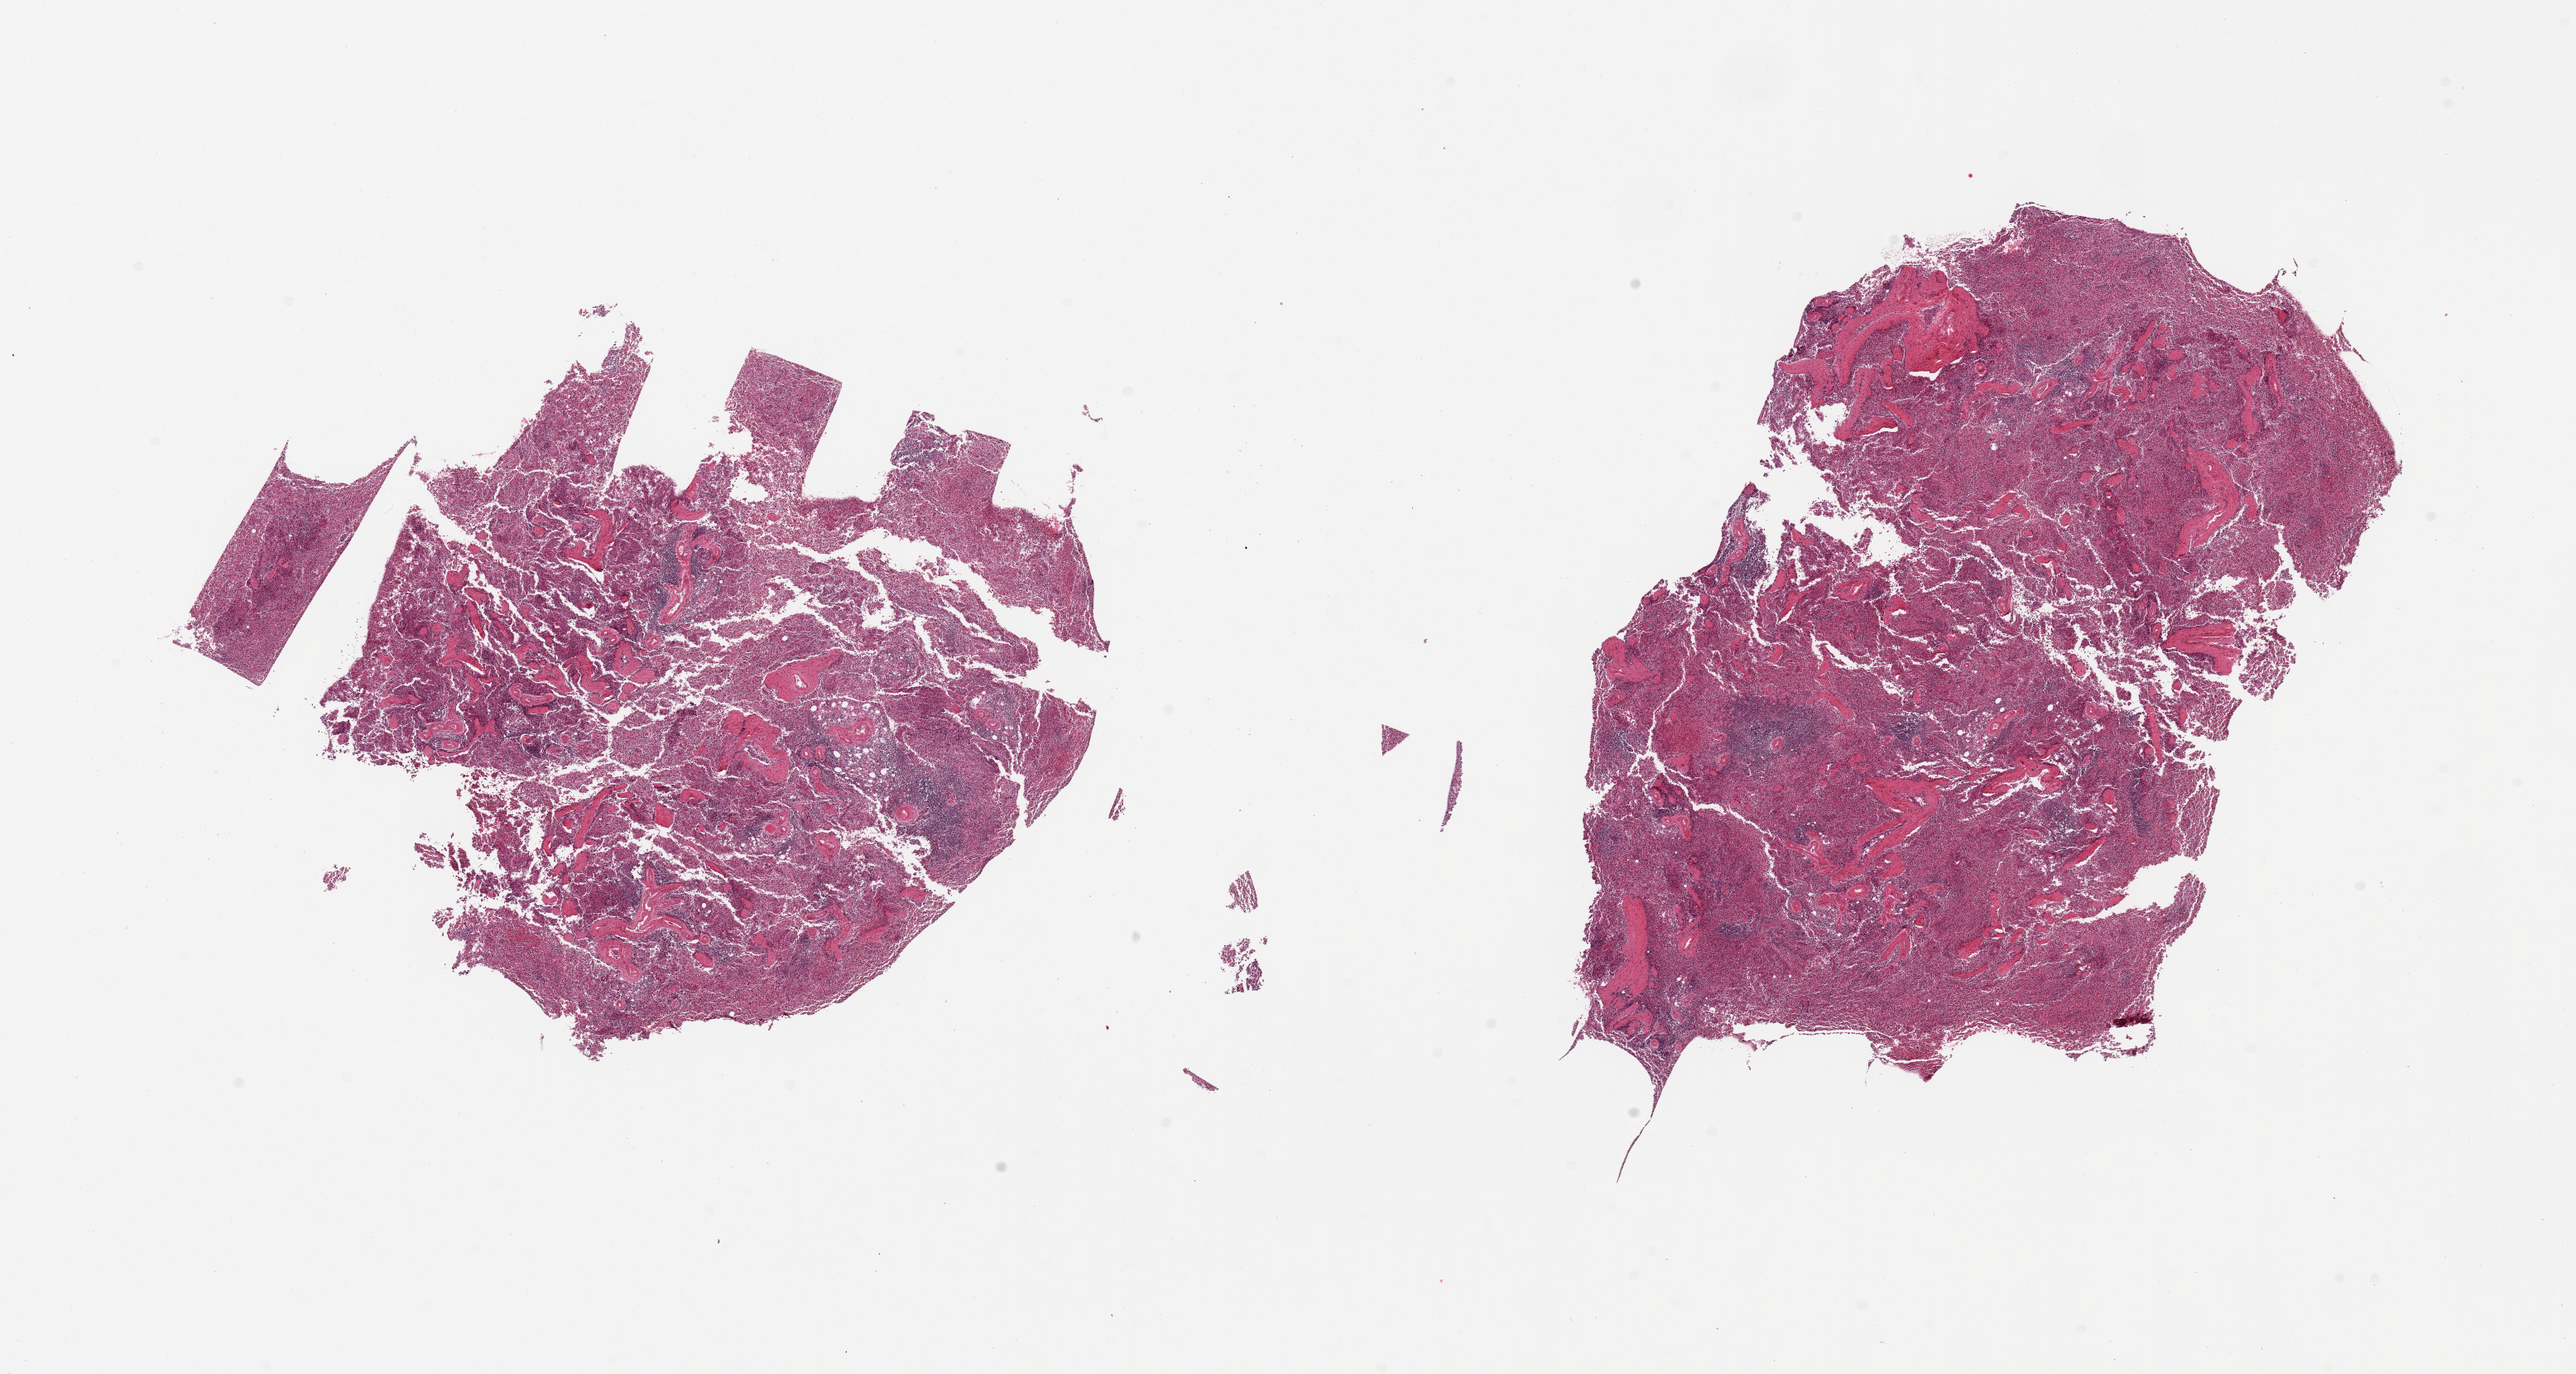
Digitized H&E-stained section, a low-resolution overview of the entire scanned area, about 24.6 x 13.1 mm (acquisition: 20x scan); PAXgene-fixed, paraffin-embedded tissue; section of spleen (target tissue); donor tissue sample.
Review note (as recorded): 2 pieces, congestion.